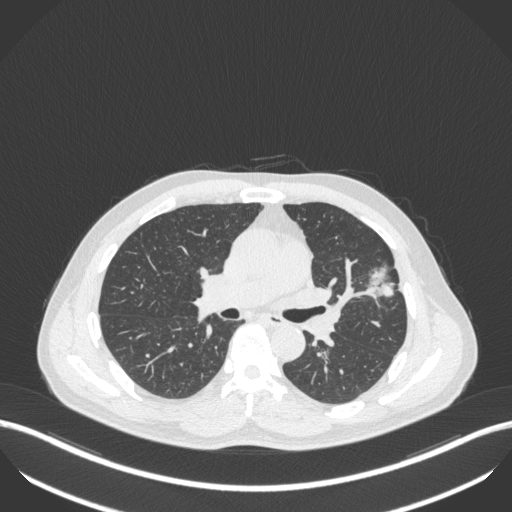
Chest CT, one axial slice; slice 229 of 418 in the series (ordered by position); reconstruction kernel B31f; 120 kVp; lung window (W 1500 / L -600 HU); 1 mm slice thickness; 512 × 512 image matrix, field of view 400 × 400 mm. Patient: male, 55 years. Case-level facts recorded for this patient, not image findings: clinical TNM (as recorded): T1c N0 M0; histopathological grade: G2-3.
Structures marked on this image (bounding box drawn by a radiologist):
- lung tumour (recorded histology: adenocarcinoma): box from (x=361, y=264) to (x=400, y=303) px